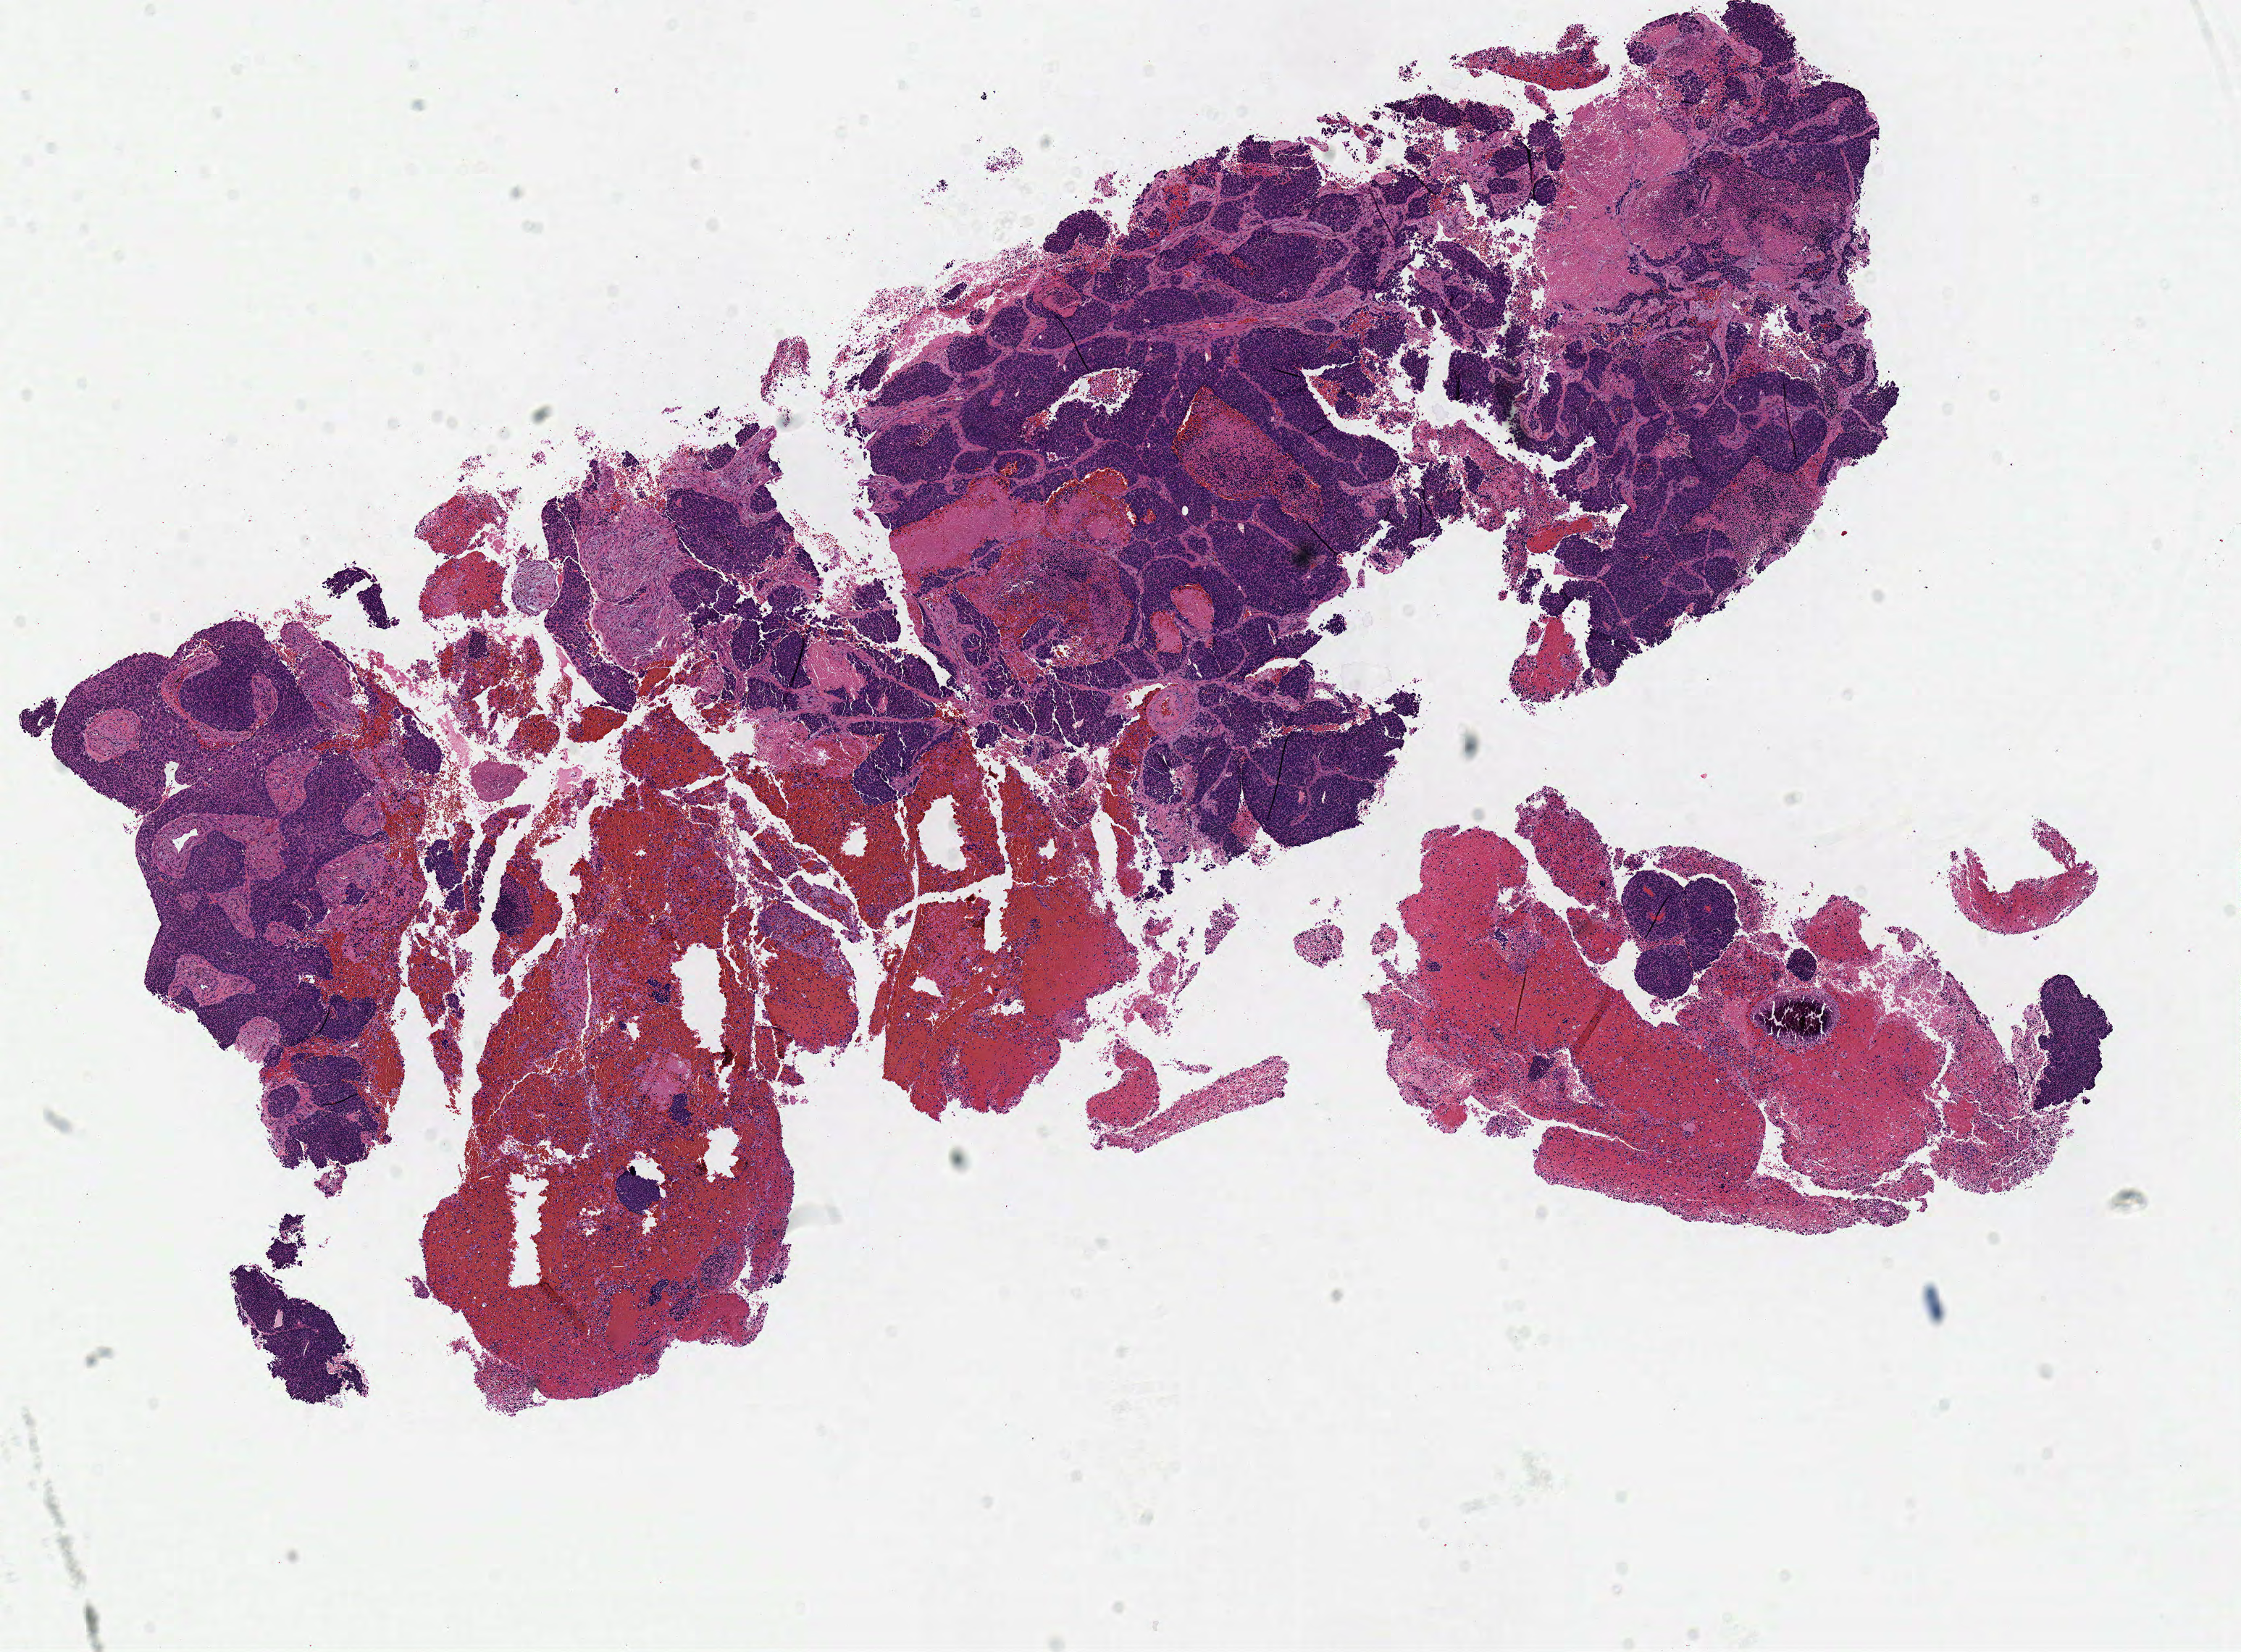
H&E-stained whole-slide image — a low-resolution overview of the entire scanned area, about 12.2 x 9.0 mm (slide scanned at 40x). Frozen section from the top of the tissue portion. Lung, primary tumour sample. Patient: male, age at initial diagnosis 70 years. Composition of this section per pathologist review: tumour cells 80%, tumour nuclei 90%, normal cells 0%, stromal cells 0%, necrosis 20%. Inflammatory infiltration, as recorded: lymphocyte infiltration 2%, monocyte infiltration 1%, neutrophil infiltration 2%.
AJCC pathologic stage: IB (7th edition). Laterality: right. Diagnosis: Basaloid squamous cell carcinoma (lower lobe, lung).